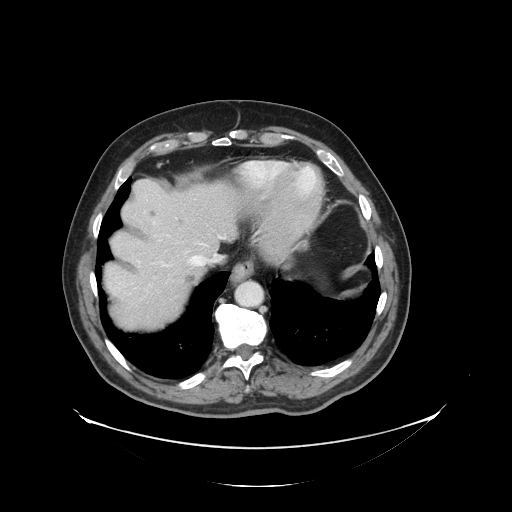
Contrast-enhanced abdominal CT, one axial slice; position 115 of 138 along the scan axis; reconstruction kernel STANDARD; intravenous contrast given; soft-tissue window (W 400 / L 40 HU); 2.5 mm slice thickness; 512 × 512 image matrix, field of view 497 × 497 mm. Male patient, age 77 years. From the clinical record (not read from this slice): diagnosis: colorectal cancer liver metastases, imaged before liver resection; multiple liver metastases: no; largest metastasis: 1.5 cm; disease in both lobes: no.
Outlined on this slice (manually delineated by an expert):
- hepatic veins: bounding box (x1, y1, x2, y2) in pixels: (136, 235, 225, 287)
- liver: (105, 180, 237, 330)
- planned liver remnant (the part of the liver to remain after resection): (105, 180, 237, 290)
- liver metastasis: (187, 277, 194, 283)
- liver metastasis: (151, 211, 157, 218)